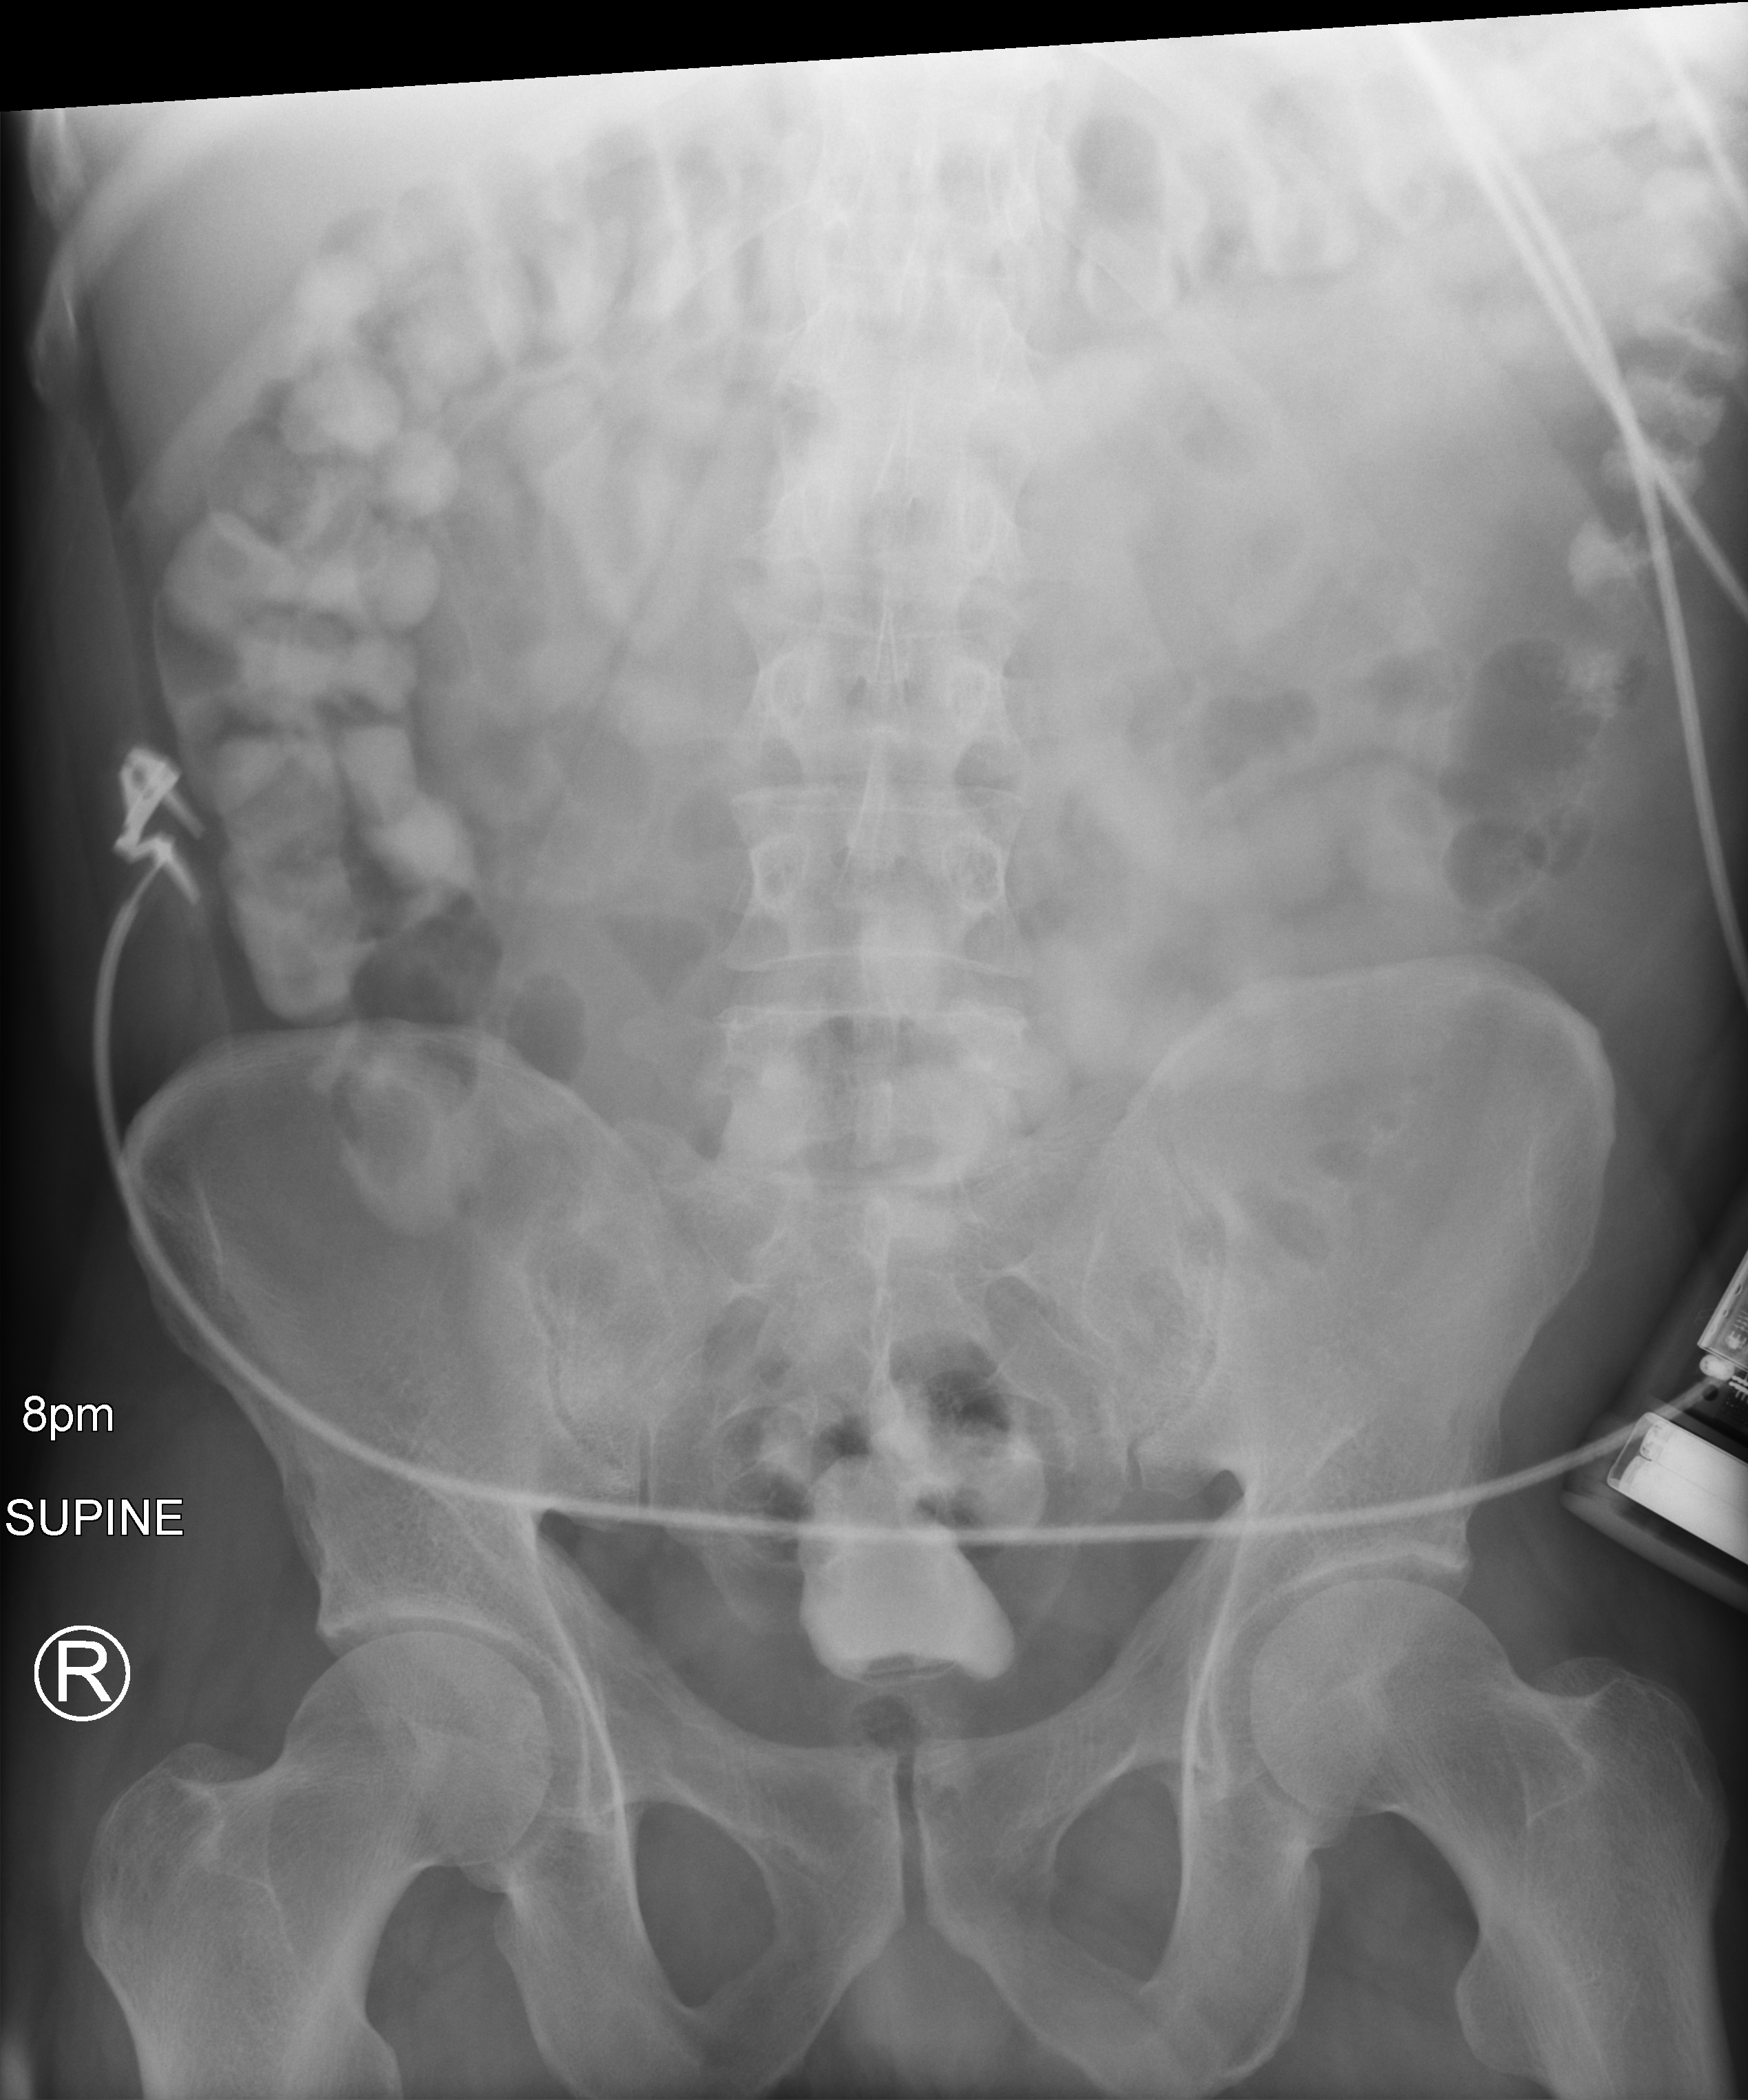
Portable abdomen radiograph, anteroposterior (AP) projection. Patient hospitalised with COVID-19; male, aged 18–59 years.
Admission-level facts for this patient (not findings on this image; timing relative to this image not recorded): admitted to intensive care during this hospital stay: no.